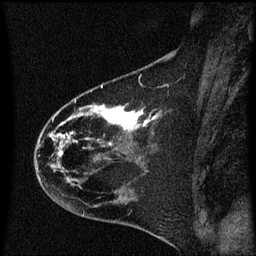
Breast MRI (dynamic contrast-enhanced), one sagittal slice; position 24 of 60 along the scan axis; dynamic contrast-enhanced series, image 2 of 3 at this slice position (ordered by acquisition); 1.5 T; TE 4.2 ms, TR 8.4 ms; 2 mm slice thickness; 256 × 256 image matrix. Patient: female, 35 years. Case-level facts recorded for this patient, not image findings: setting: breast cancer imaged before/during neoadjuvant chemotherapy; receptor status: HER2-positive.
Structures marked on this image (semi-automatic segmentation, software-assisted and operator-edited):
- analysis volume of interest (the breast-tissue region the enhancement analysis was run in; not a lesion): box from (x=35, y=68) to (x=174, y=173) px
- tumour enhancement mask (voxels above the 70 % enhancement threshold inside the analysis volume of interest): (x=50, y=108)–(x=158, y=157)